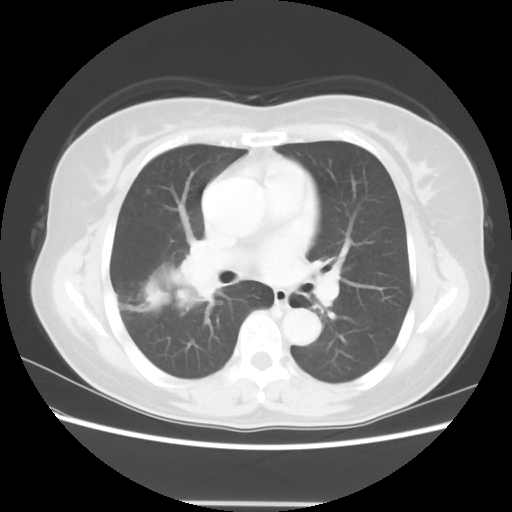
Chest CT, one axial slice; position 33 of 56 along the scan axis; lung window (W 1500 / L -600 HU); 5 mm slice thickness; 512 × 512 image matrix. Female patient, age 55 years. Case-level facts recorded for this patient, not image findings: clinical TNM (as recorded): T2 N1 M0; histopathological grade: G2-3.
Outlined on this slice (rectangle marked by the reading radiologist):
- lung tumour (recorded histology: adenocarcinoma): bounding box [x1, y1, x2, y2] px = [126, 253, 225, 329]